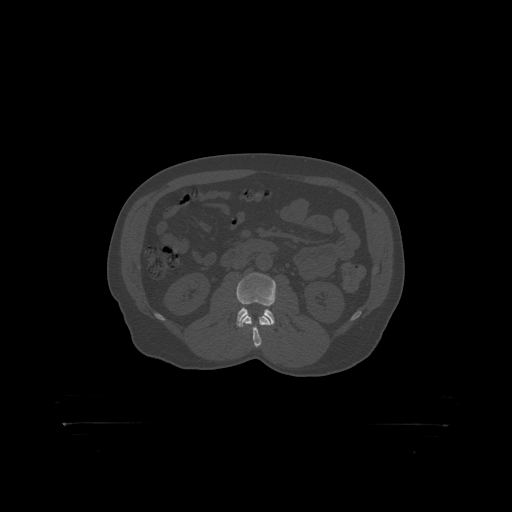
CT including the spine, one axial slice; position 280 of 399 along the scan axis; bone window (W 1800 / L 400 HU); 1.25 mm slice thickness; 512 × 512 image matrix, field of view 650 × 650 mm. Male patient, age 46 years. Case-level facts recorded for this patient, not image findings: primary cancer: skin.
Outlined on this slice (semi-automatic segmentation, software-assisted and operator-edited):
- L2 vertebra: bounding box <243,315,266,319> (left, top, right, bottom; pixels)
- L3 vertebra: <237,273,277,319>